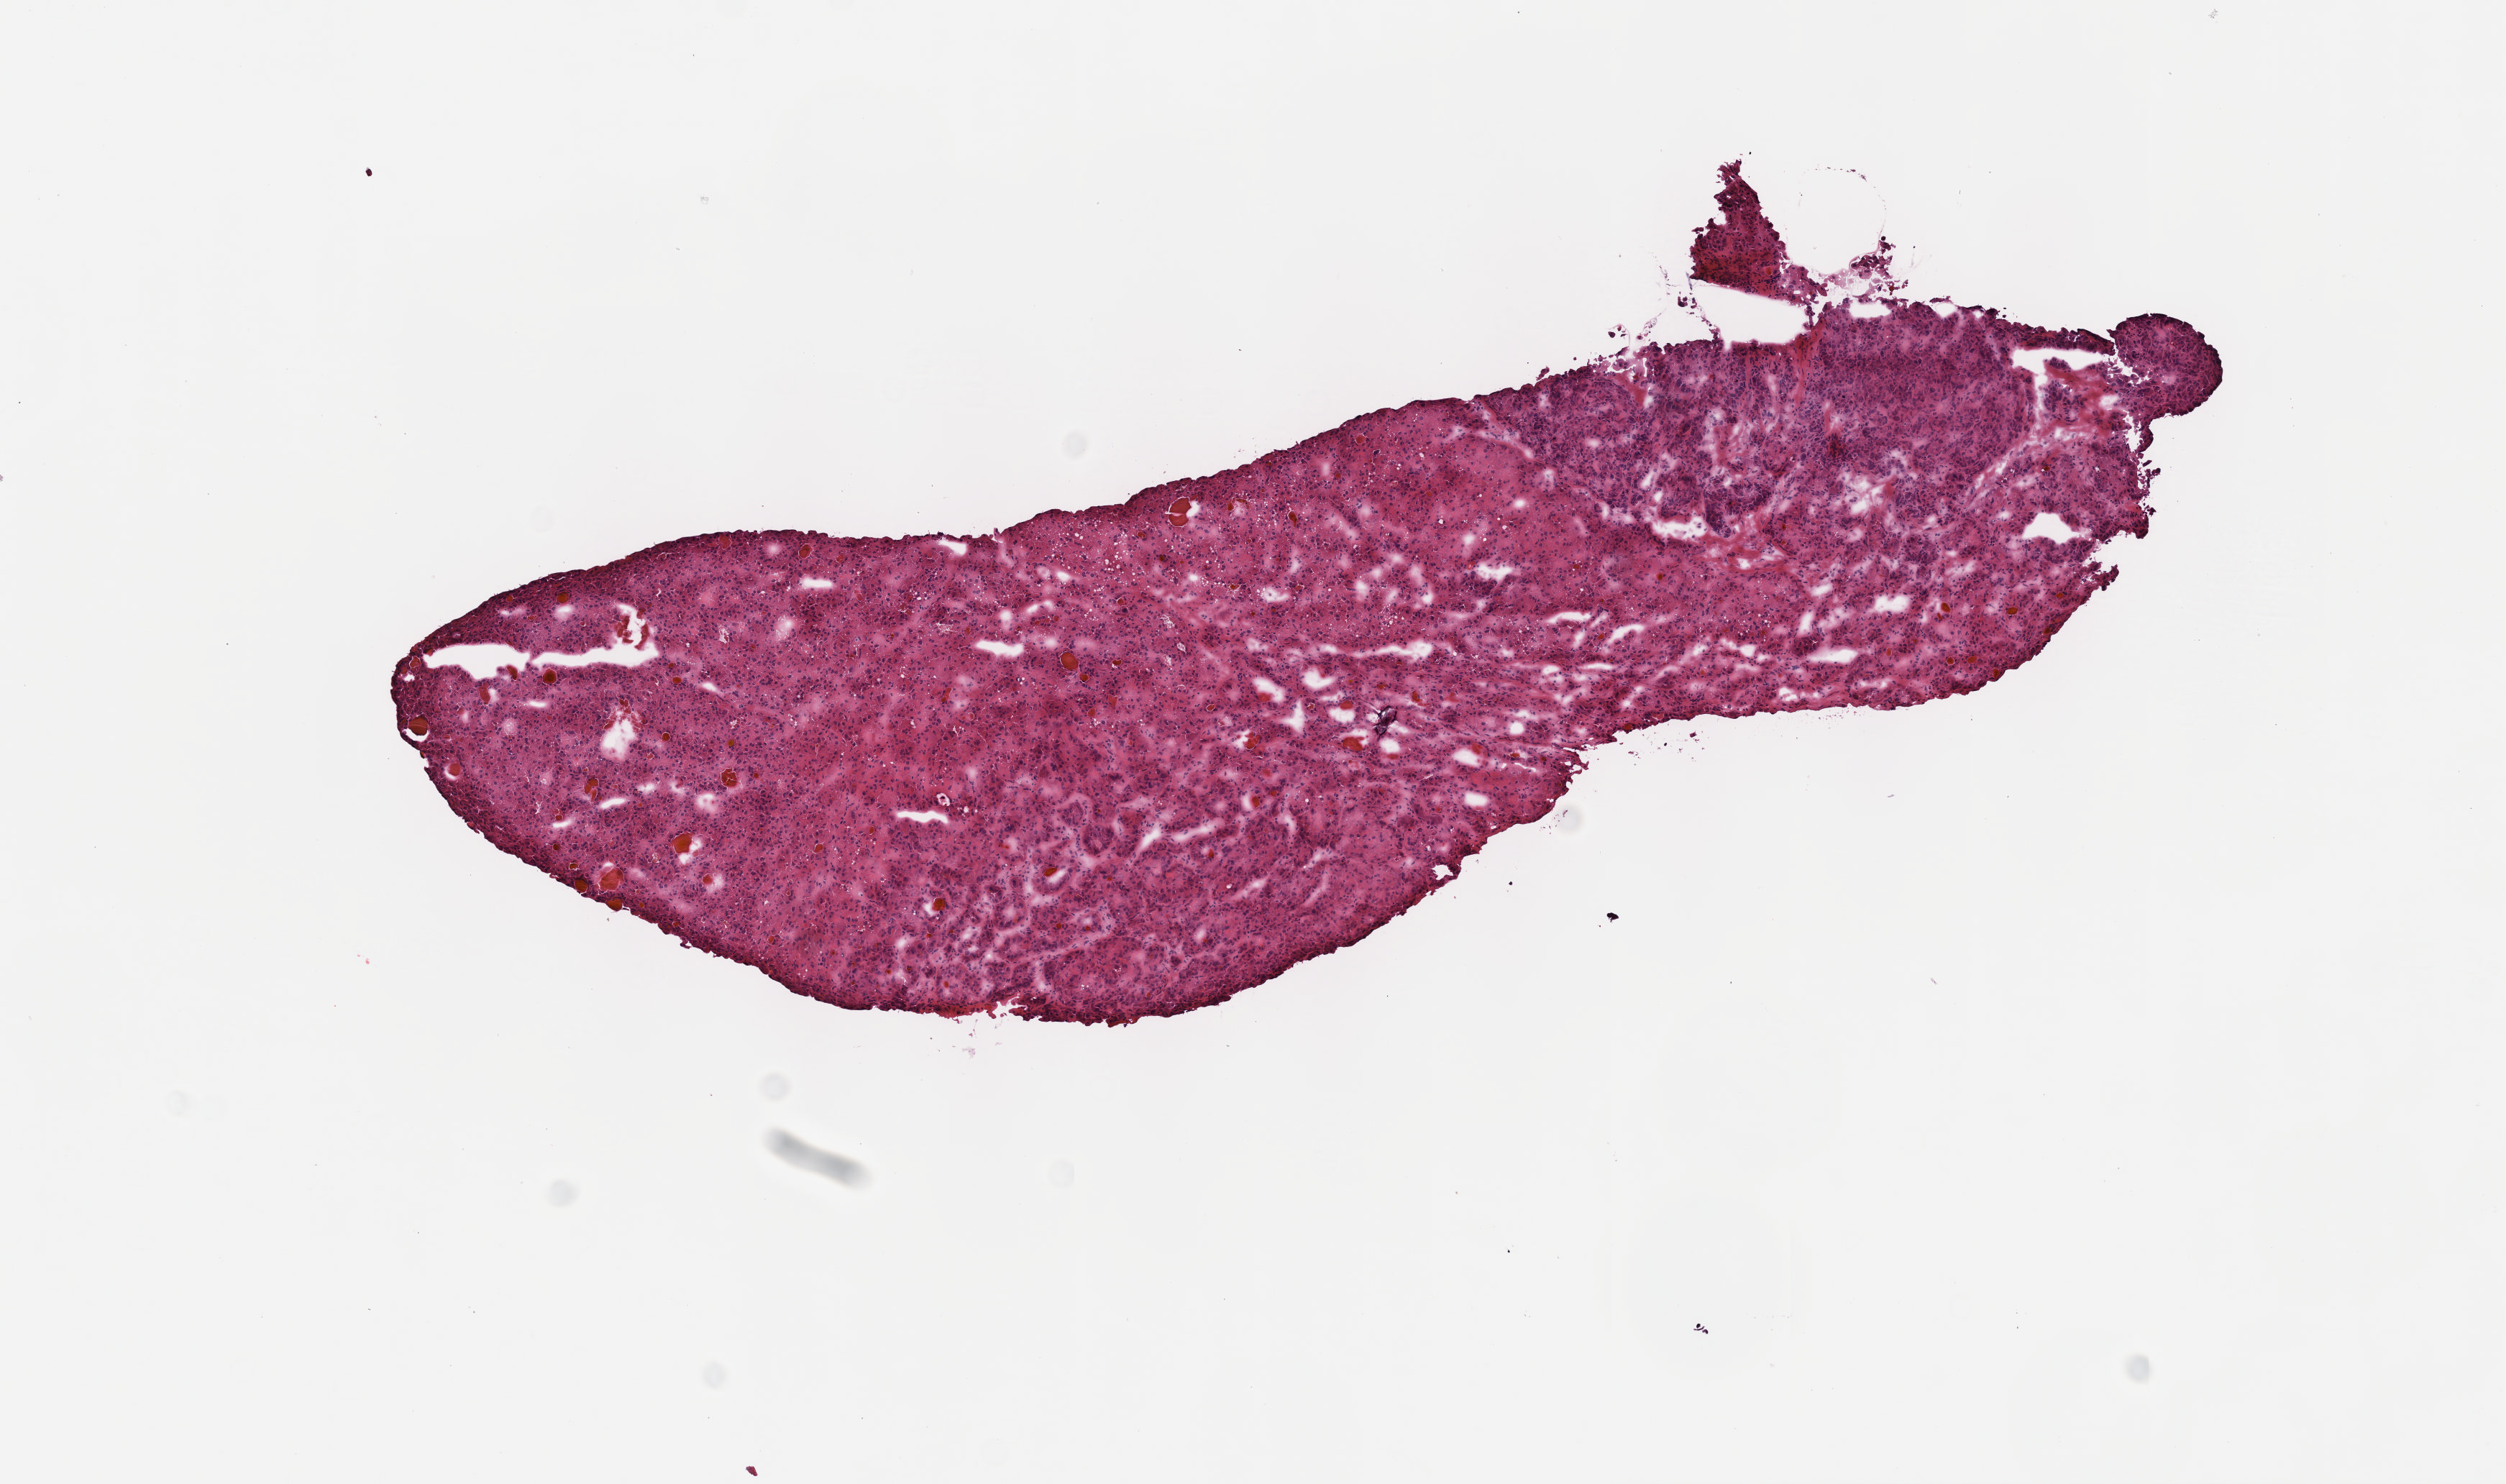
H&E-stained whole-slide image — a low-resolution overview of the entire scanned area, about 7.0 x 4.2 mm, frozen section from the top of the tissue portion, primary tumour sample from the liver. Female, age 59 years at initial diagnosis. Histologic grade: G3 (poorly differentiated). Slide review estimates, as recorded: tumour cells 100%, tumour nuclei 80%, normal cells 0%, stromal cells 0%, necrosis 0%. Infiltration values recorded for this section: lymphocyte infiltration 2%, monocyte infiltration 0%, neutrophil infiltration 0%.
- diagnosis: Hepatocellular carcinoma, NOS
- AJCC pathologic stage: I (7th edition)
- TNM: T1 N0 M0